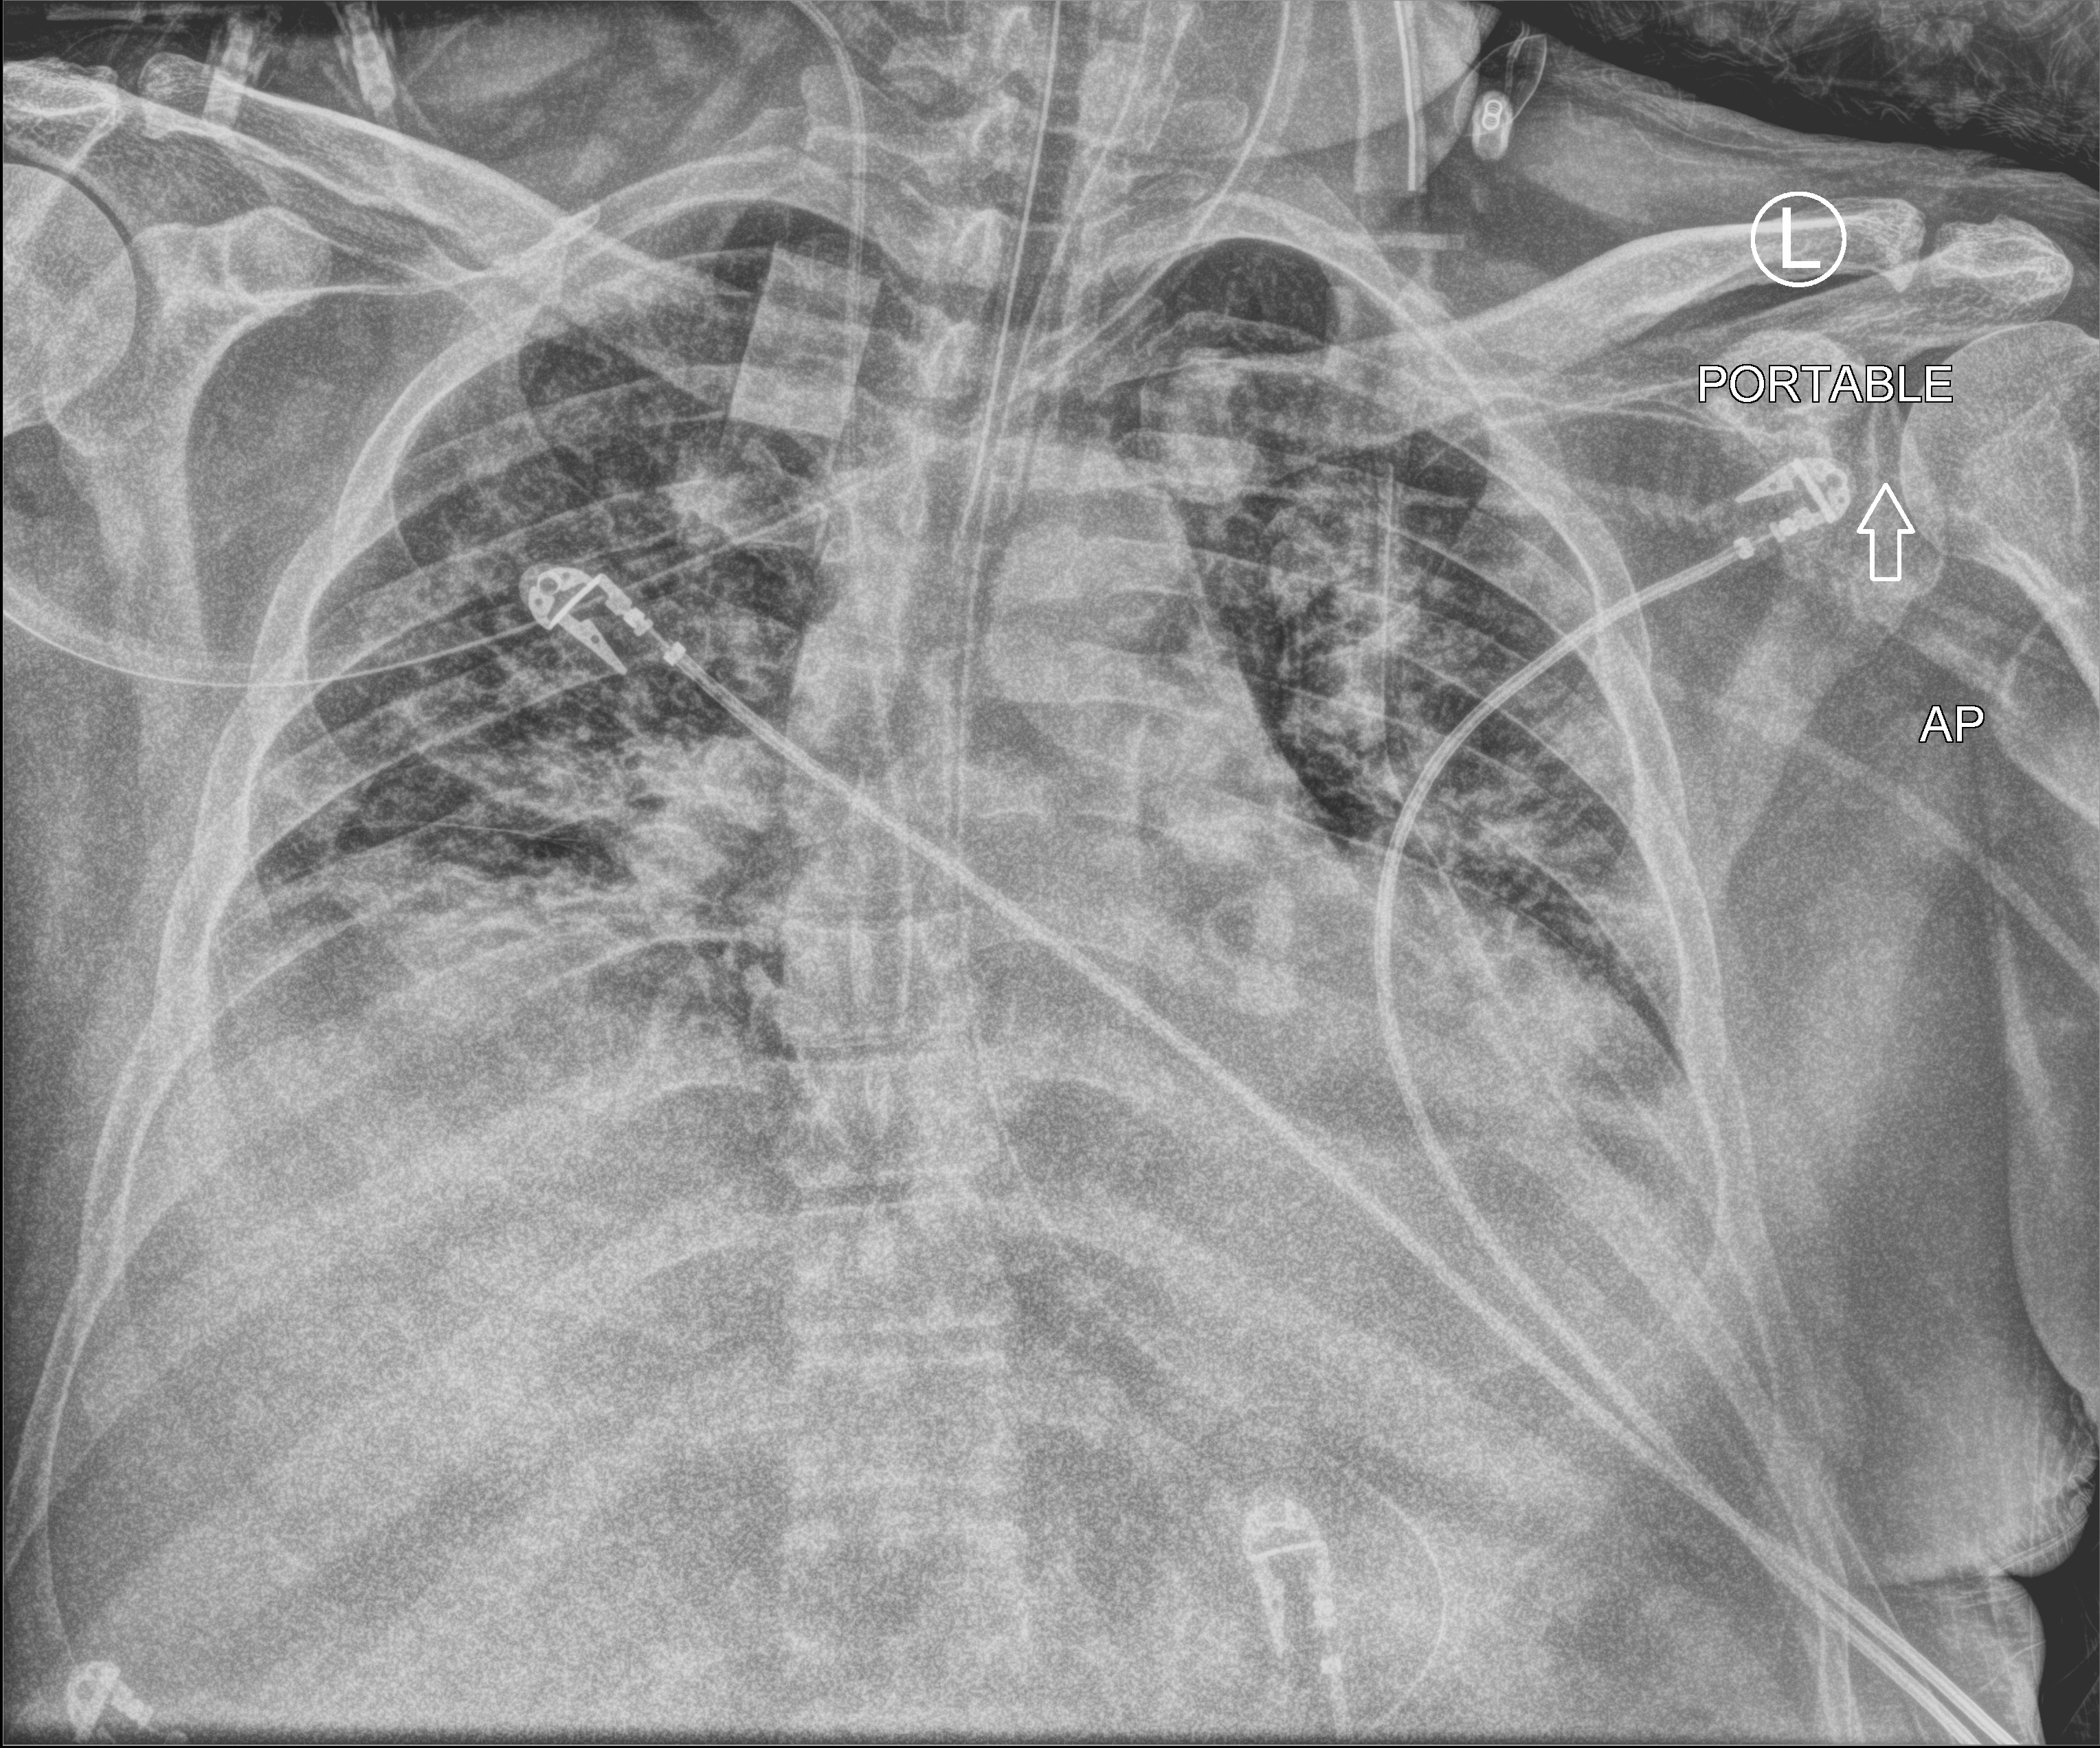
Bedside chest radiograph (computed radiography); anteroposterior (AP) projection. Male patient hospitalised with COVID-19, age 18–59 years.
Hospital-stay facts (about this admission, not read from this image; timing relative to this image not recorded):
- admitted to intensive care during this hospital stay: yes